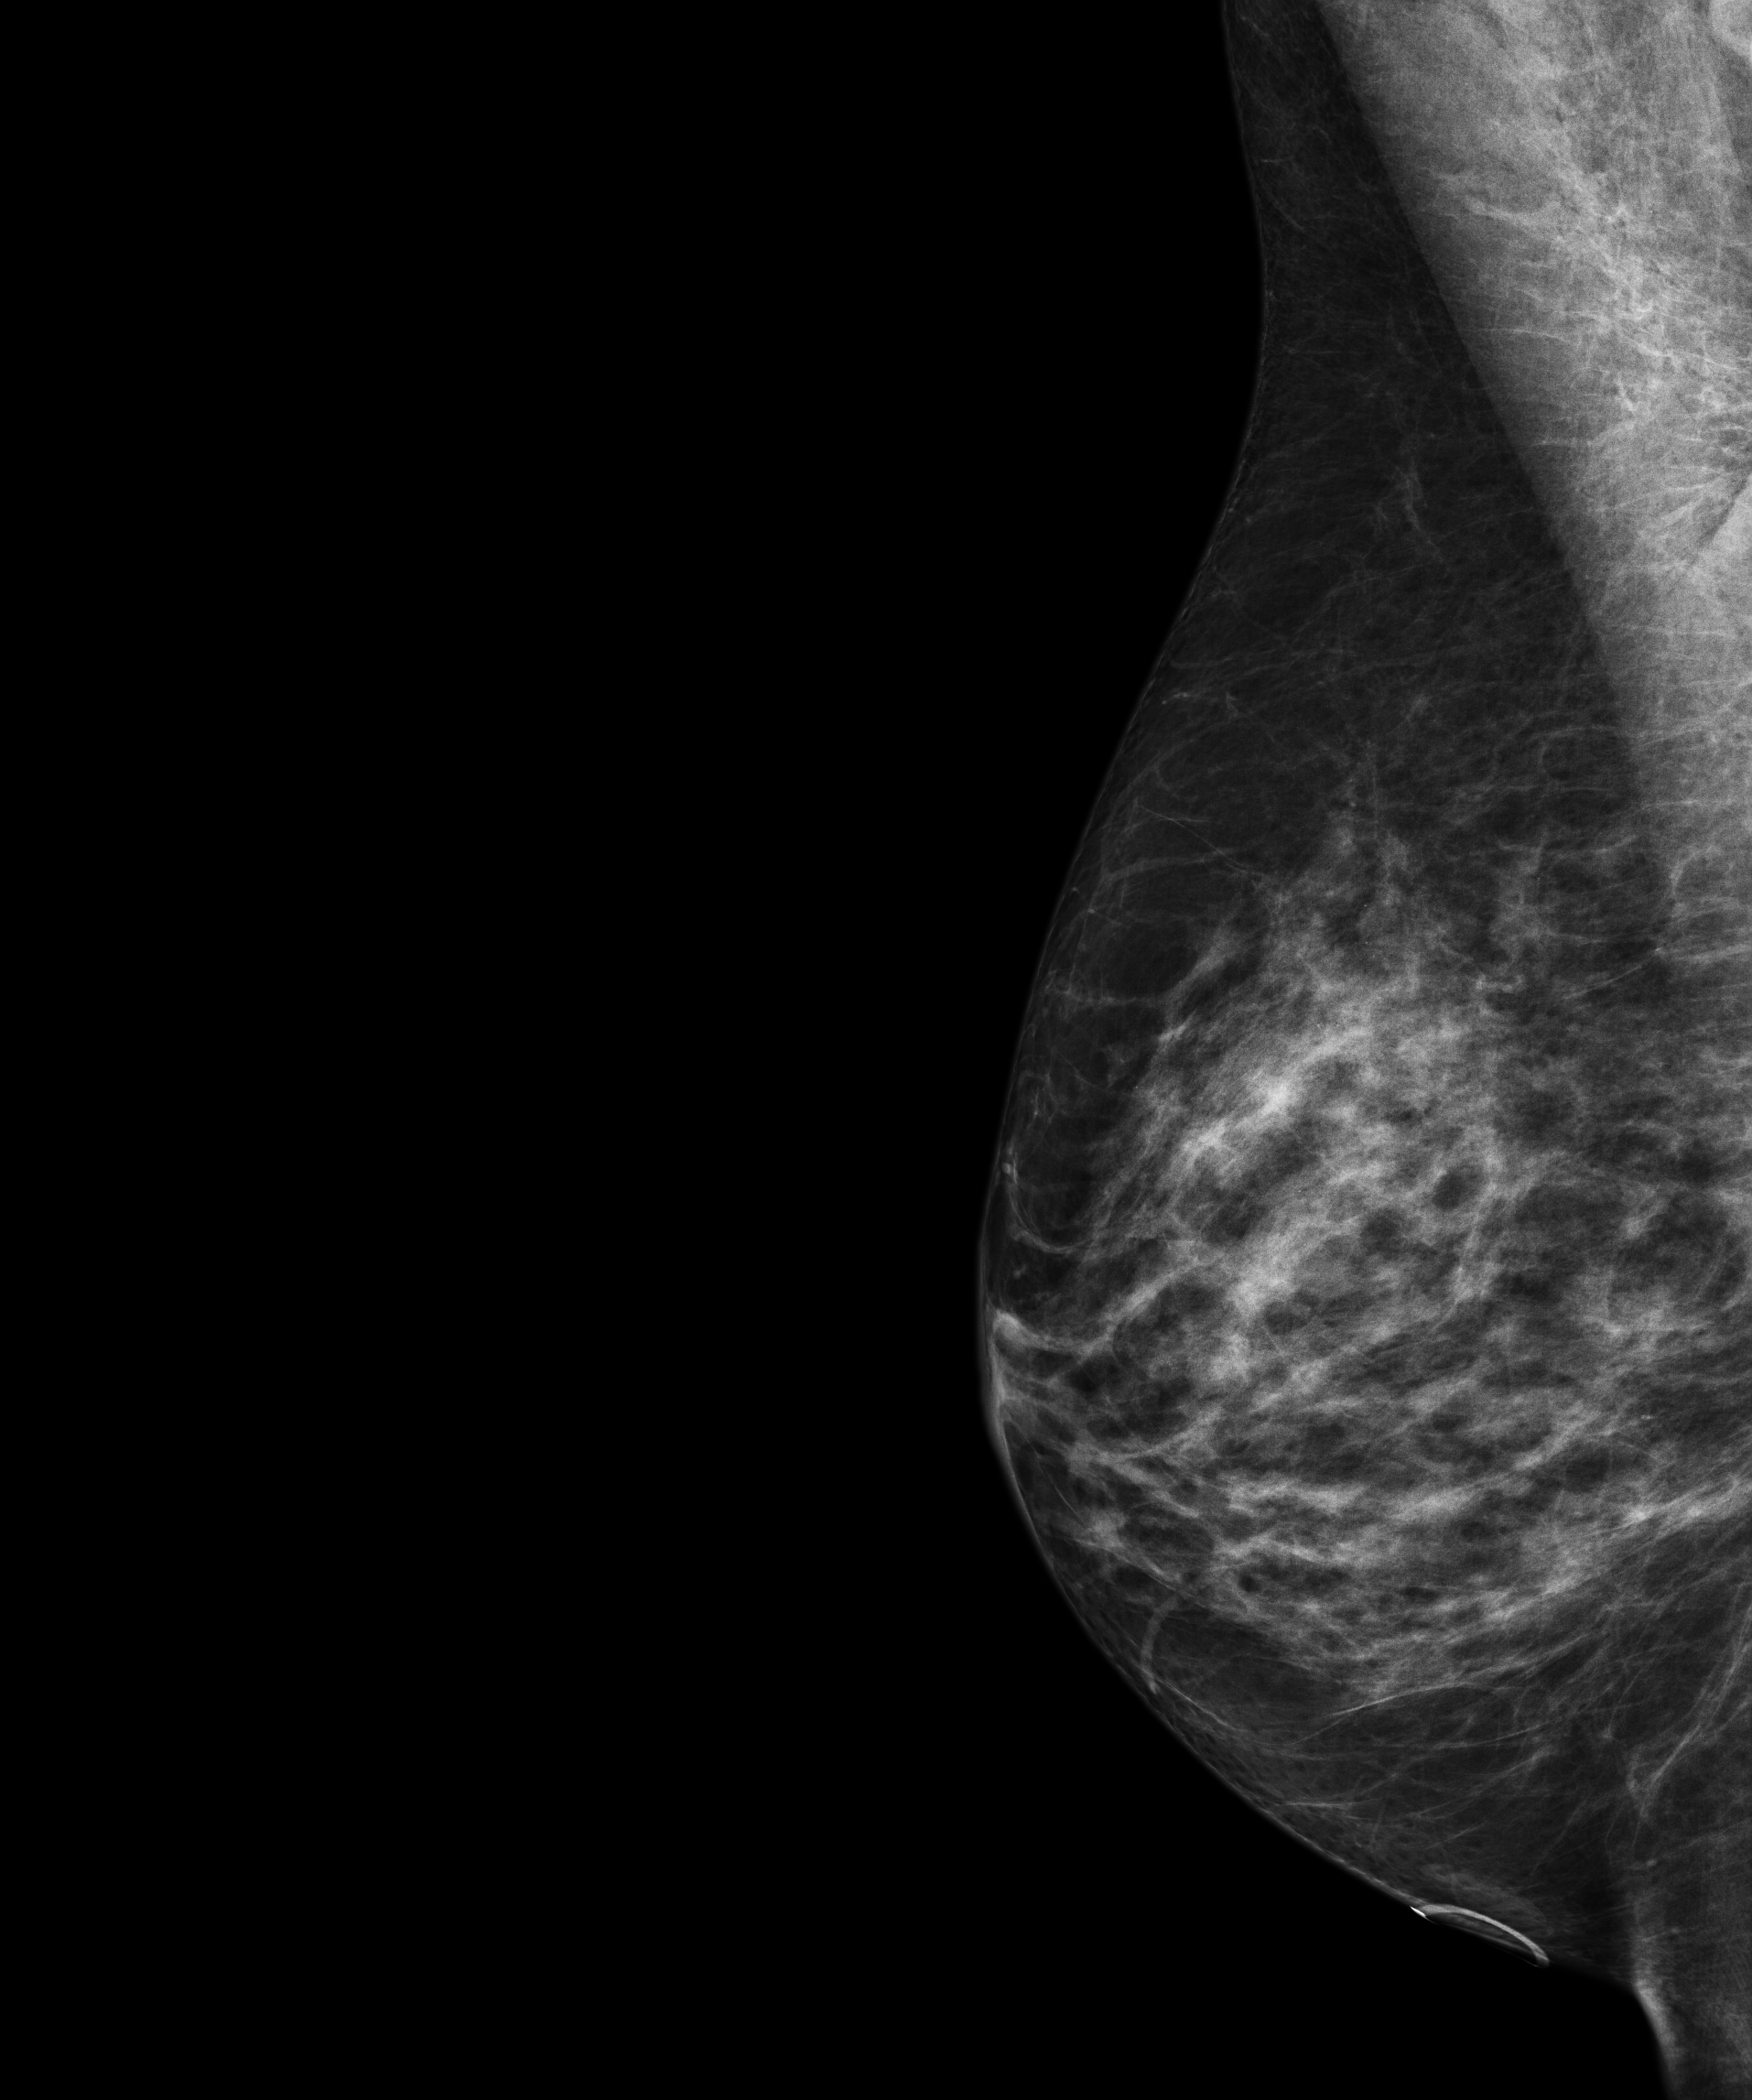
Full-field digital mammogram (FFDM), right breast, mediolateral oblique (MLO) view, annual screening mammography examination. Female patient, age 58 years.
- breast density at the screening exam (both breasts): heterogeneously dense (BI-RADS density category c)
- final BI-RADS assessment for this screening round (tomosynthesis exam, both breasts): category 1
- recall: no recall after this screen